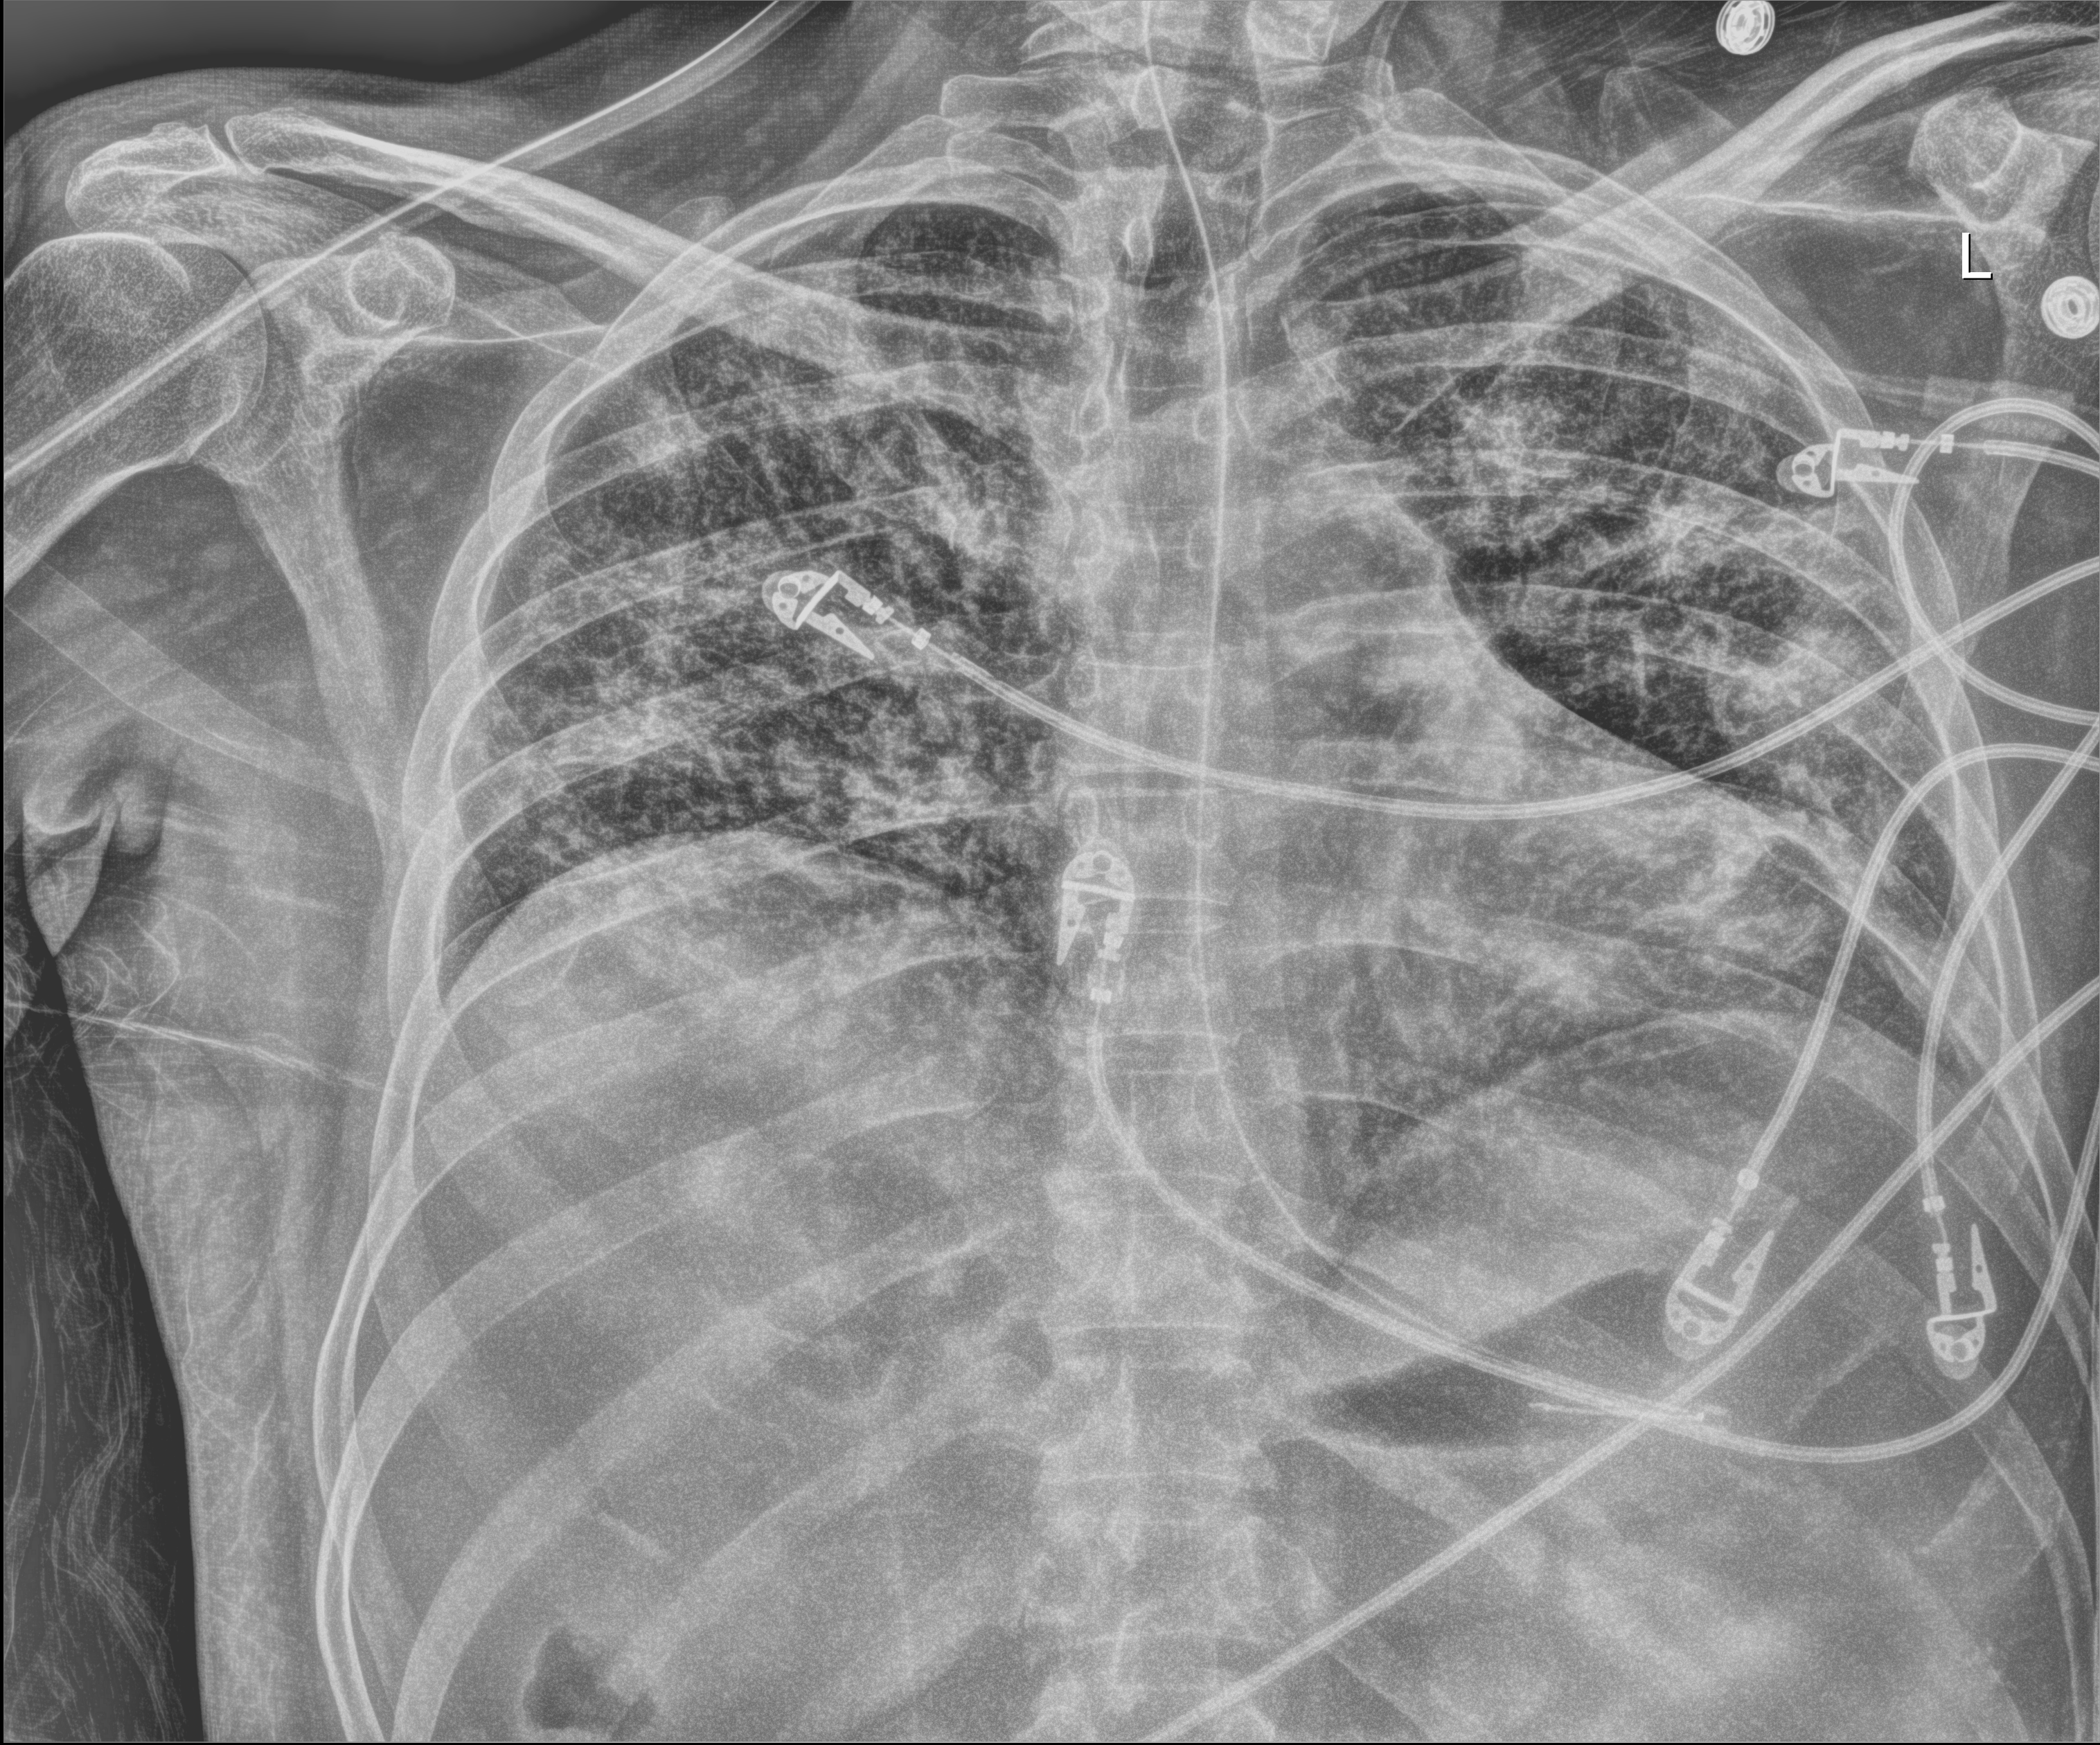
Chest X-ray (portable), anteroposterior (AP) projection. Patient hospitalised with COVID-19; male, aged 18–59 years.
Admission-level facts for this patient (not findings on this image; timing relative to this image not recorded):
- length of hospital stay: 48 days
- COPD (admission record): no